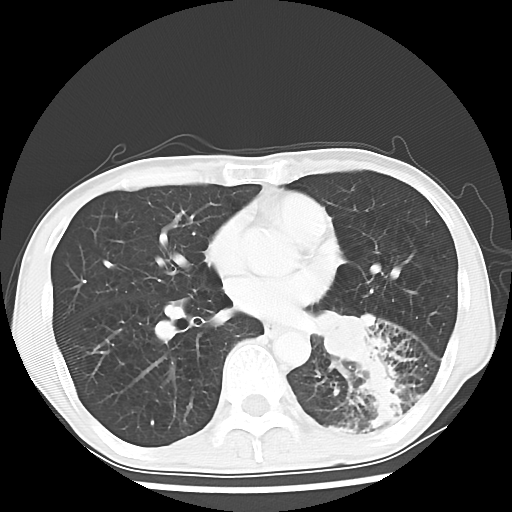
Chest CT, one axial slice; slice 29 of 64 in the series (ordered by position); 120 kVp; lung window (W 1500 / L -600 HU); 512 × 512 image matrix. Male patient, age 68 years. Case-level facts recorded for this patient, not image findings: clinical TNM (as recorded): T4 N0 M0.
Structures marked on this image (bounding box drawn by a radiologist):
- lung tumour (recorded histology: squamous cell carcinoma): box from (x=316, y=312) to (x=375, y=367) px